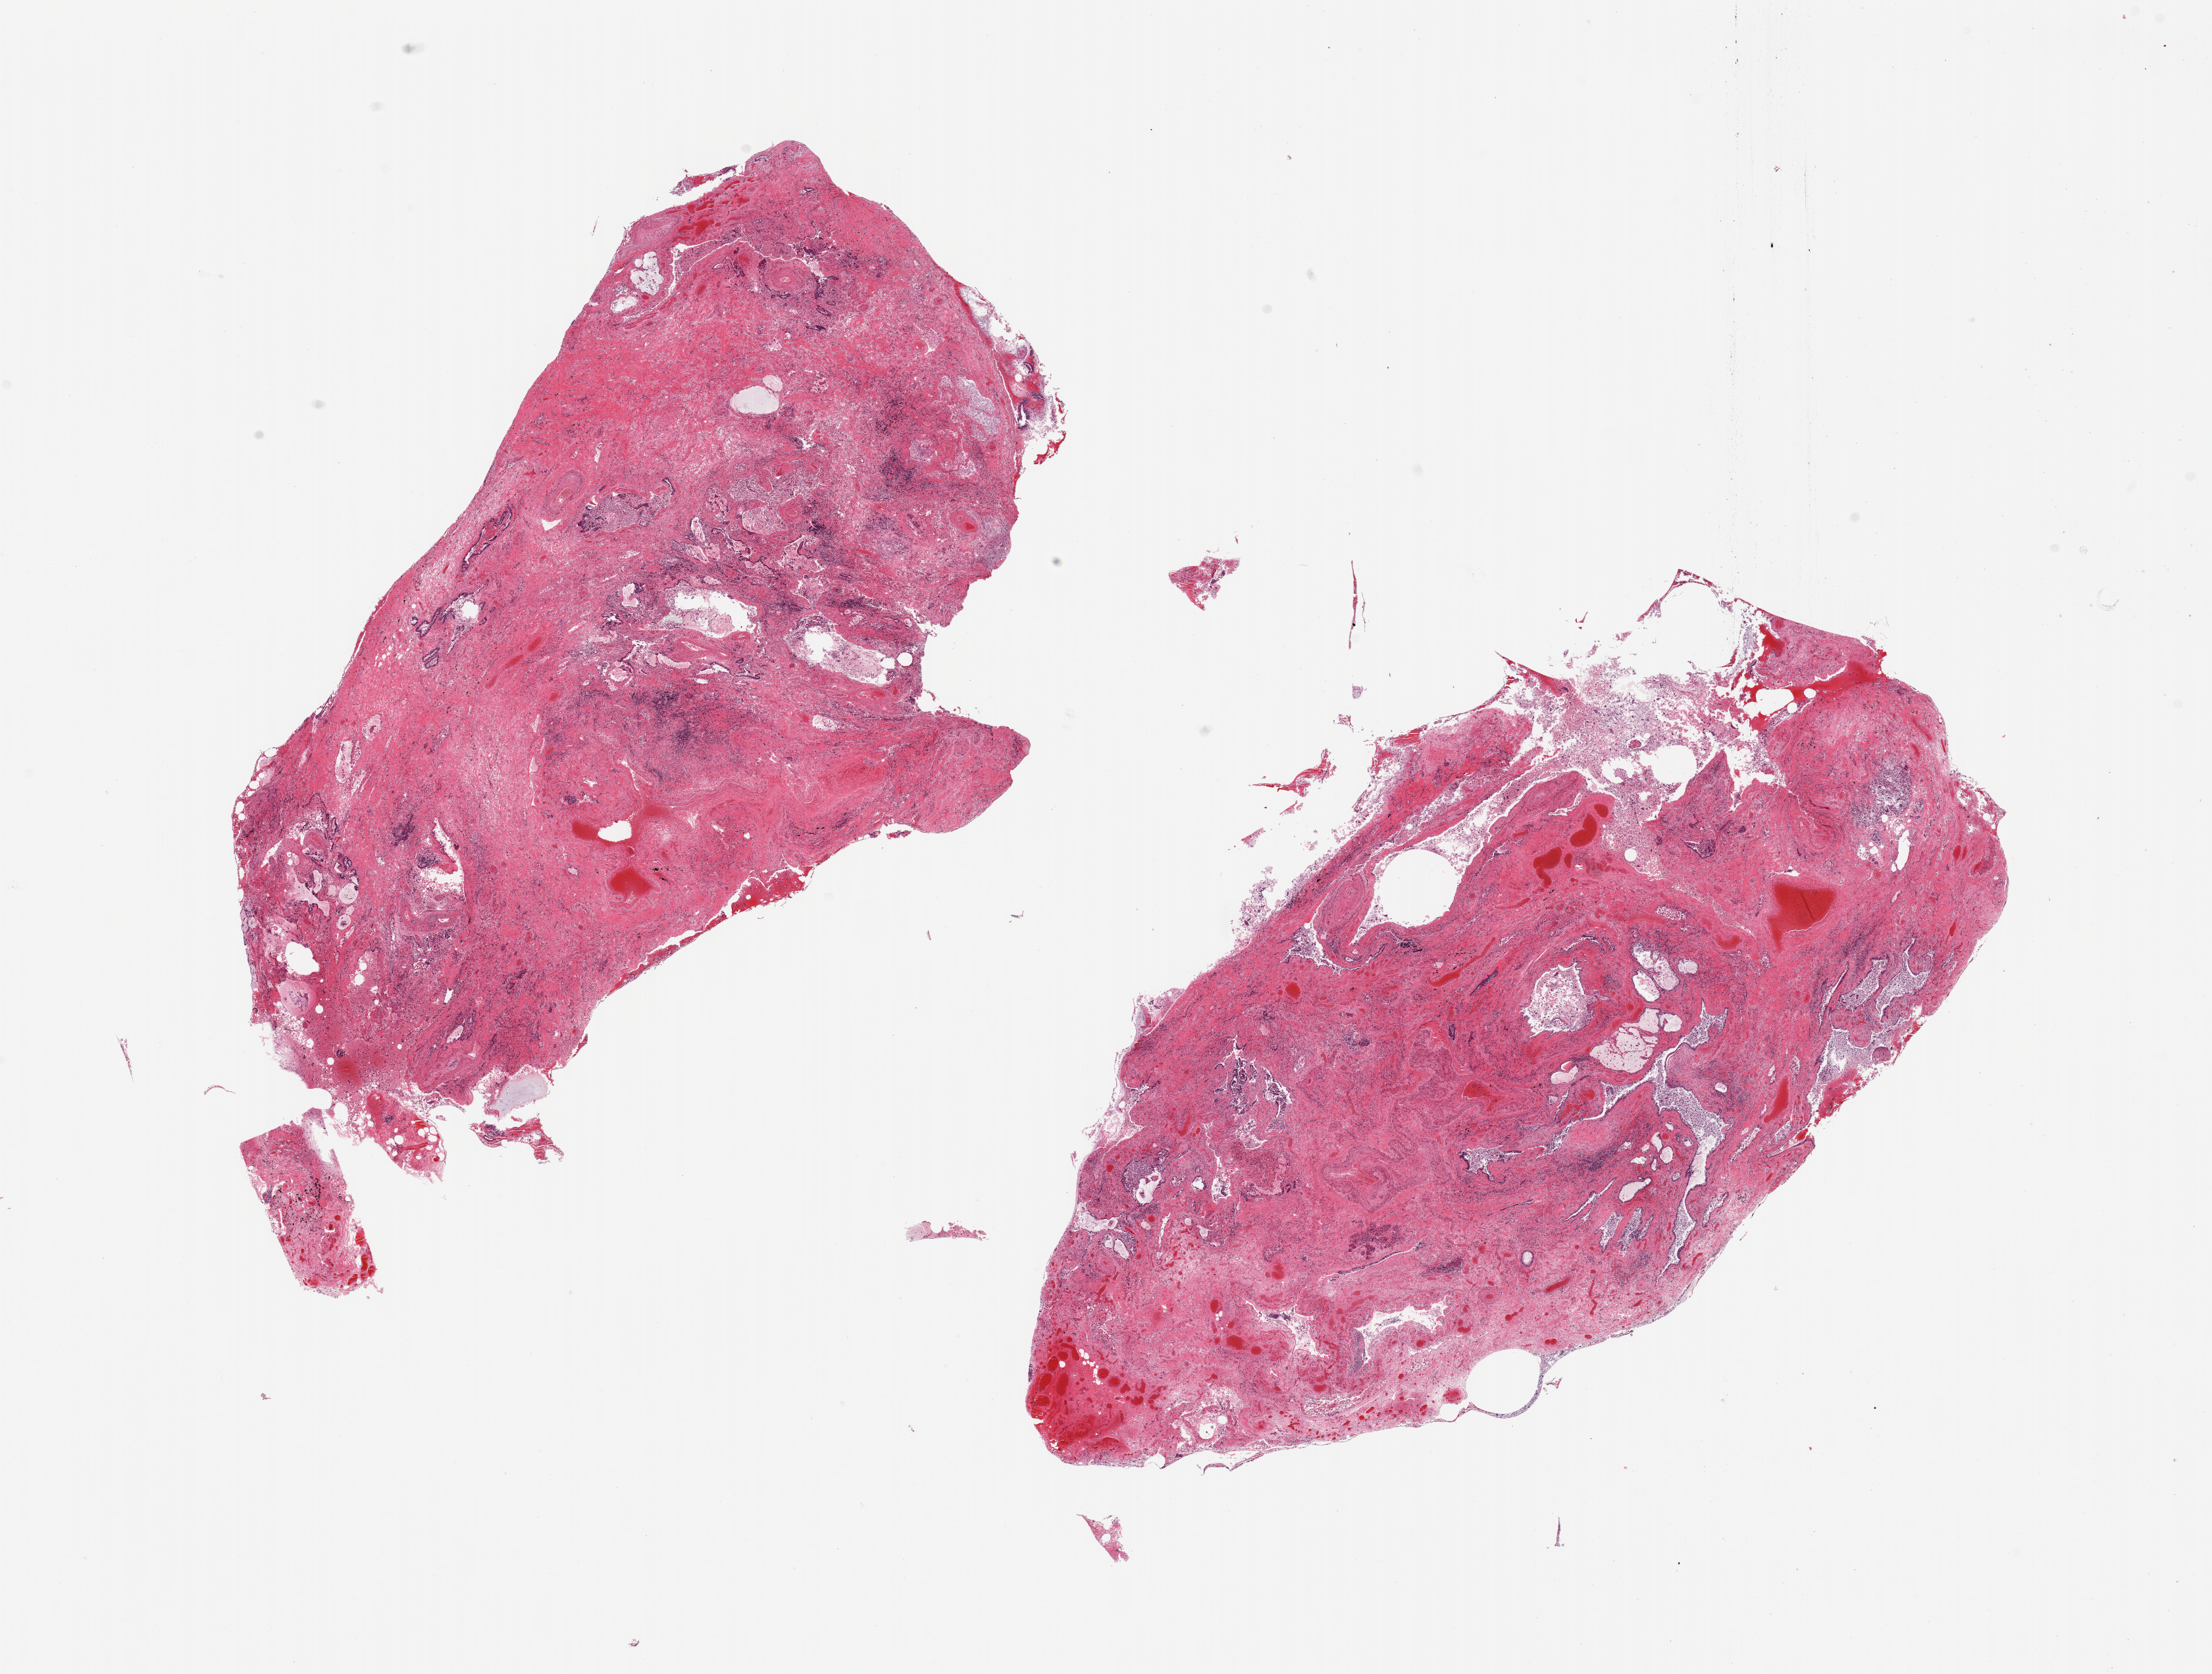
Digitized haematoxylin and eosin-stained section, a low-resolution overview of the entire scanned area, about 26.6 x 20.1 mm (acquisition: 20x scan); PAXgene-fixed, paraffin-embedded tissue; section of lung (target tissue); donor tissue sample. Donor sex: male.
* pathologist's review note for this sample: 2 pieces; bronchiectasis, bronchitis, extensive fibrosis; no normal lung parenchyma